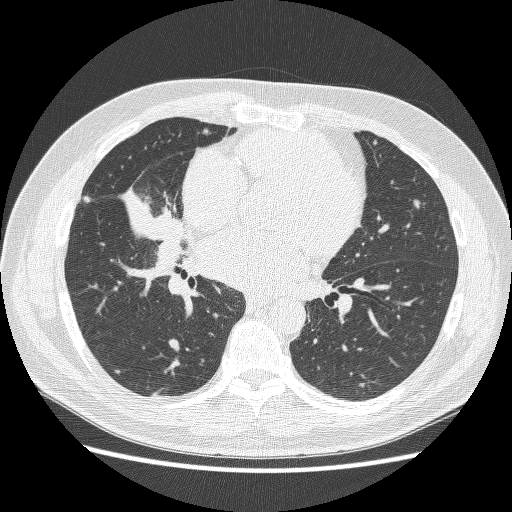
Axial slice from a low-dose chest CT screening exam. Baseline annual screen. Lung window (W 1500 / L -600 HU). 512 × 512 image matrix. Male, age 59 years at enrolment.
• Lesion marked by an expert reader, bounding box (x1, y1, x2, y2) in pixels: (114, 170, 196, 252).
• Screening reader's record for this exam: no non-calcified nodule ≥4 mm recorded.
• Official screen result: positive, change unspecified: nodule(s) >= 4 mm or enlarging nodule(s), mass(es), or other non-specific abnormalities suspicious for lung cancer.
• Later outcome: lung cancer diagnosed 24 days after this screen — adenocarcinoma, NOS, right middle lobe, poorly differentiated (G3), stage IV (AJCC 6th edition), 54 mm at pathology.